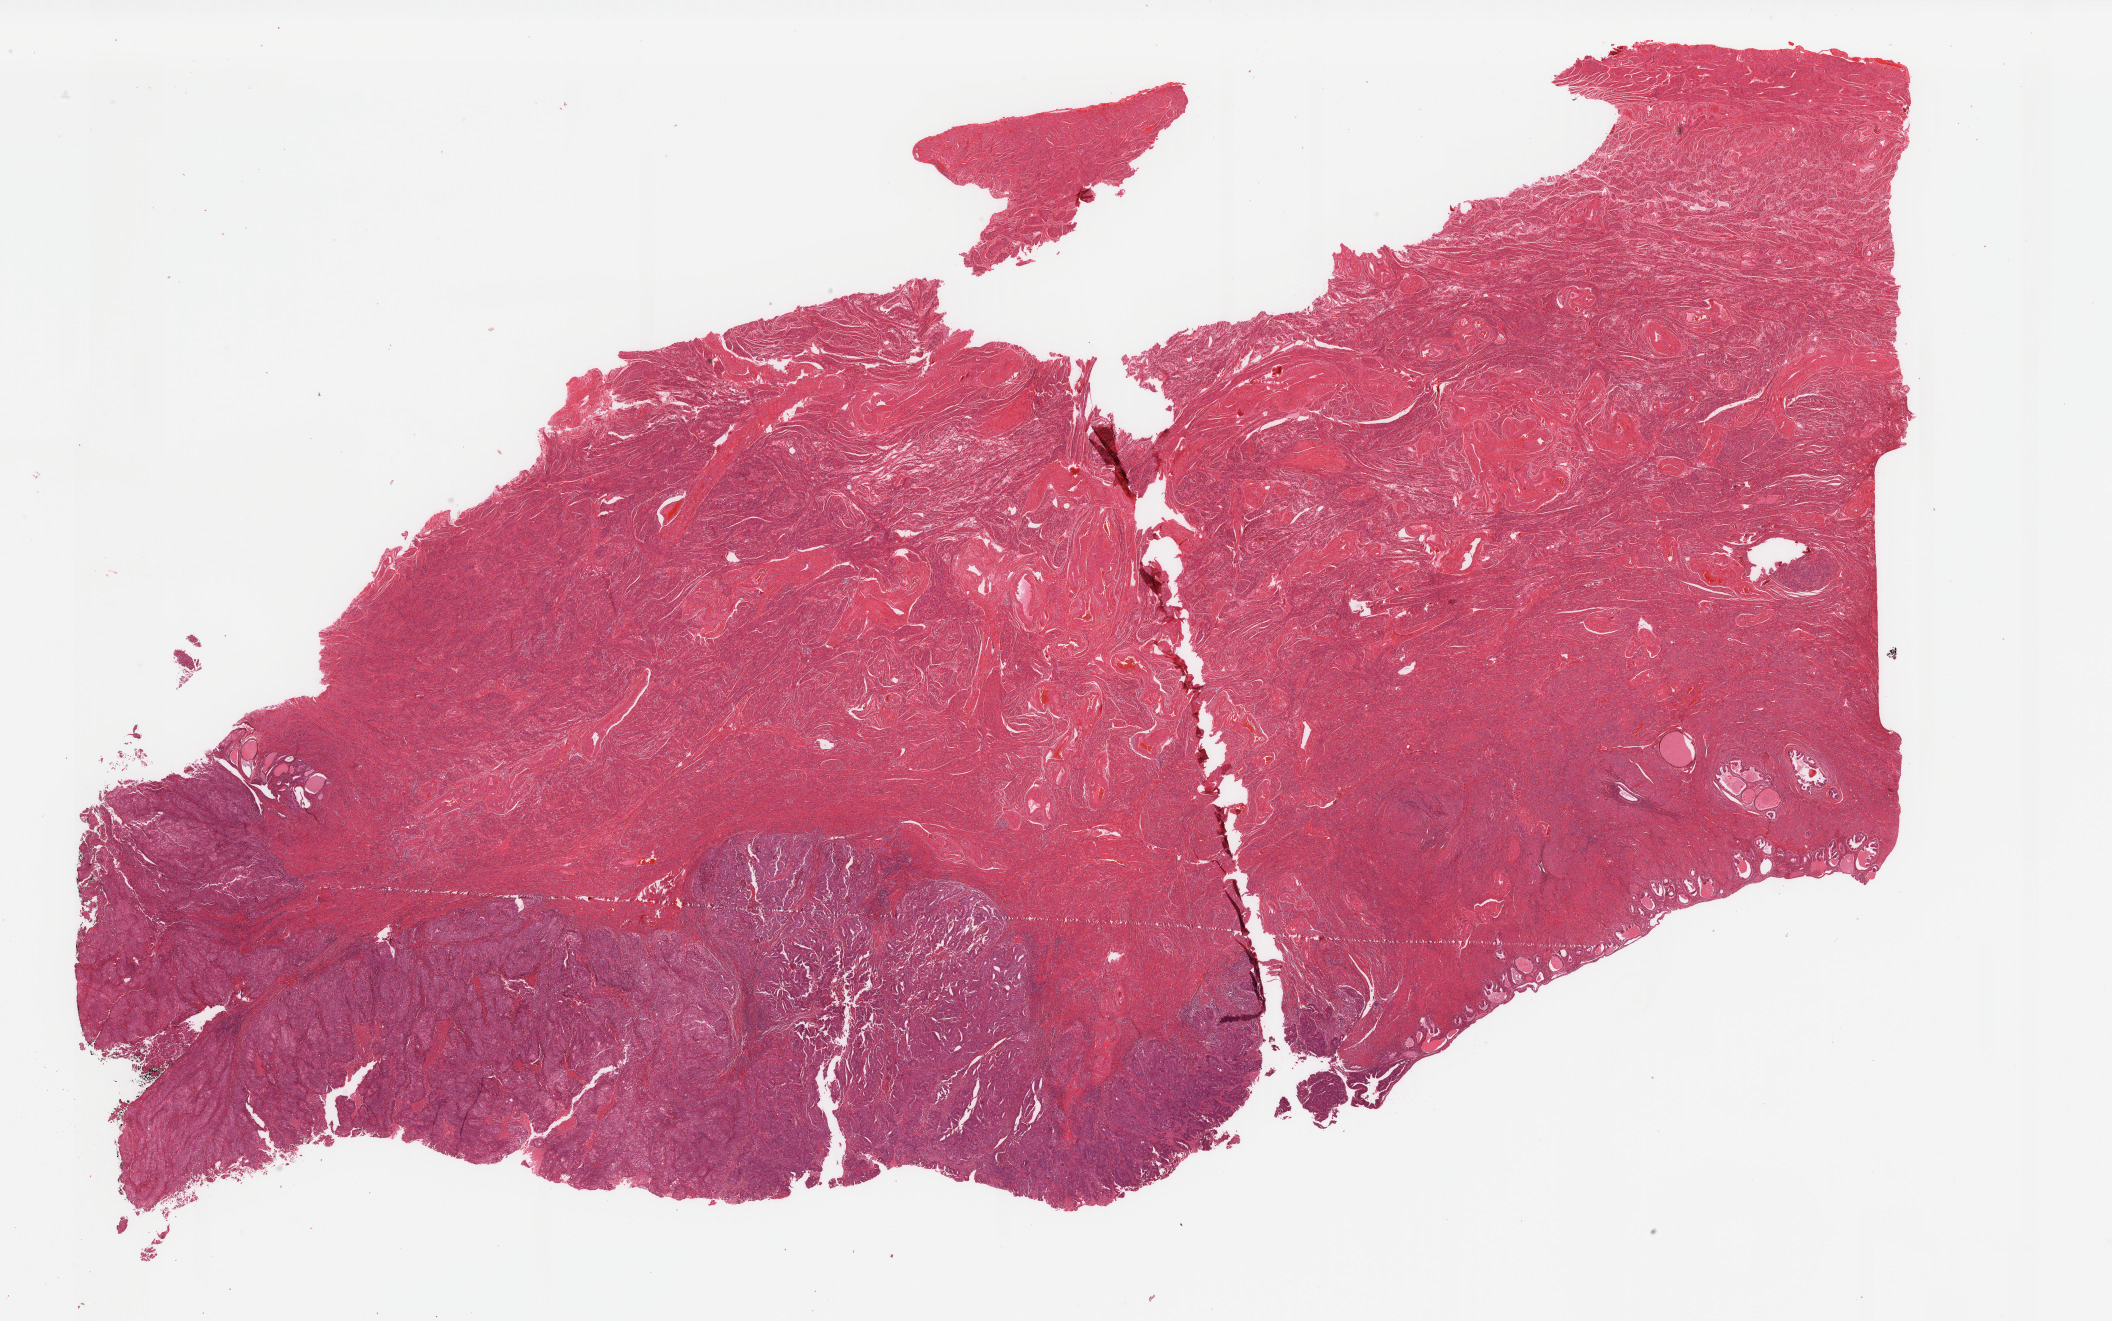
Whole-slide histology image, Hematoxylin and eosin (H&E) stained — a low-resolution overview of the entire scanned area, about 33.5 x 21.0 mm (from a 40x scan); formalin-fixed paraffin-embedded (FFPE) diagnostic section; sample: primary tumour, uterus. Female, age 80 years at initial diagnosis. Histologic grade: G2 (moderately differentiated).
• FIGO stage: IB
• lymph nodes positive (case pathology): 0 of 7 examined
• pathologic diagnosis: Endometrioid adenocarcinoma, NOS (endometrium)